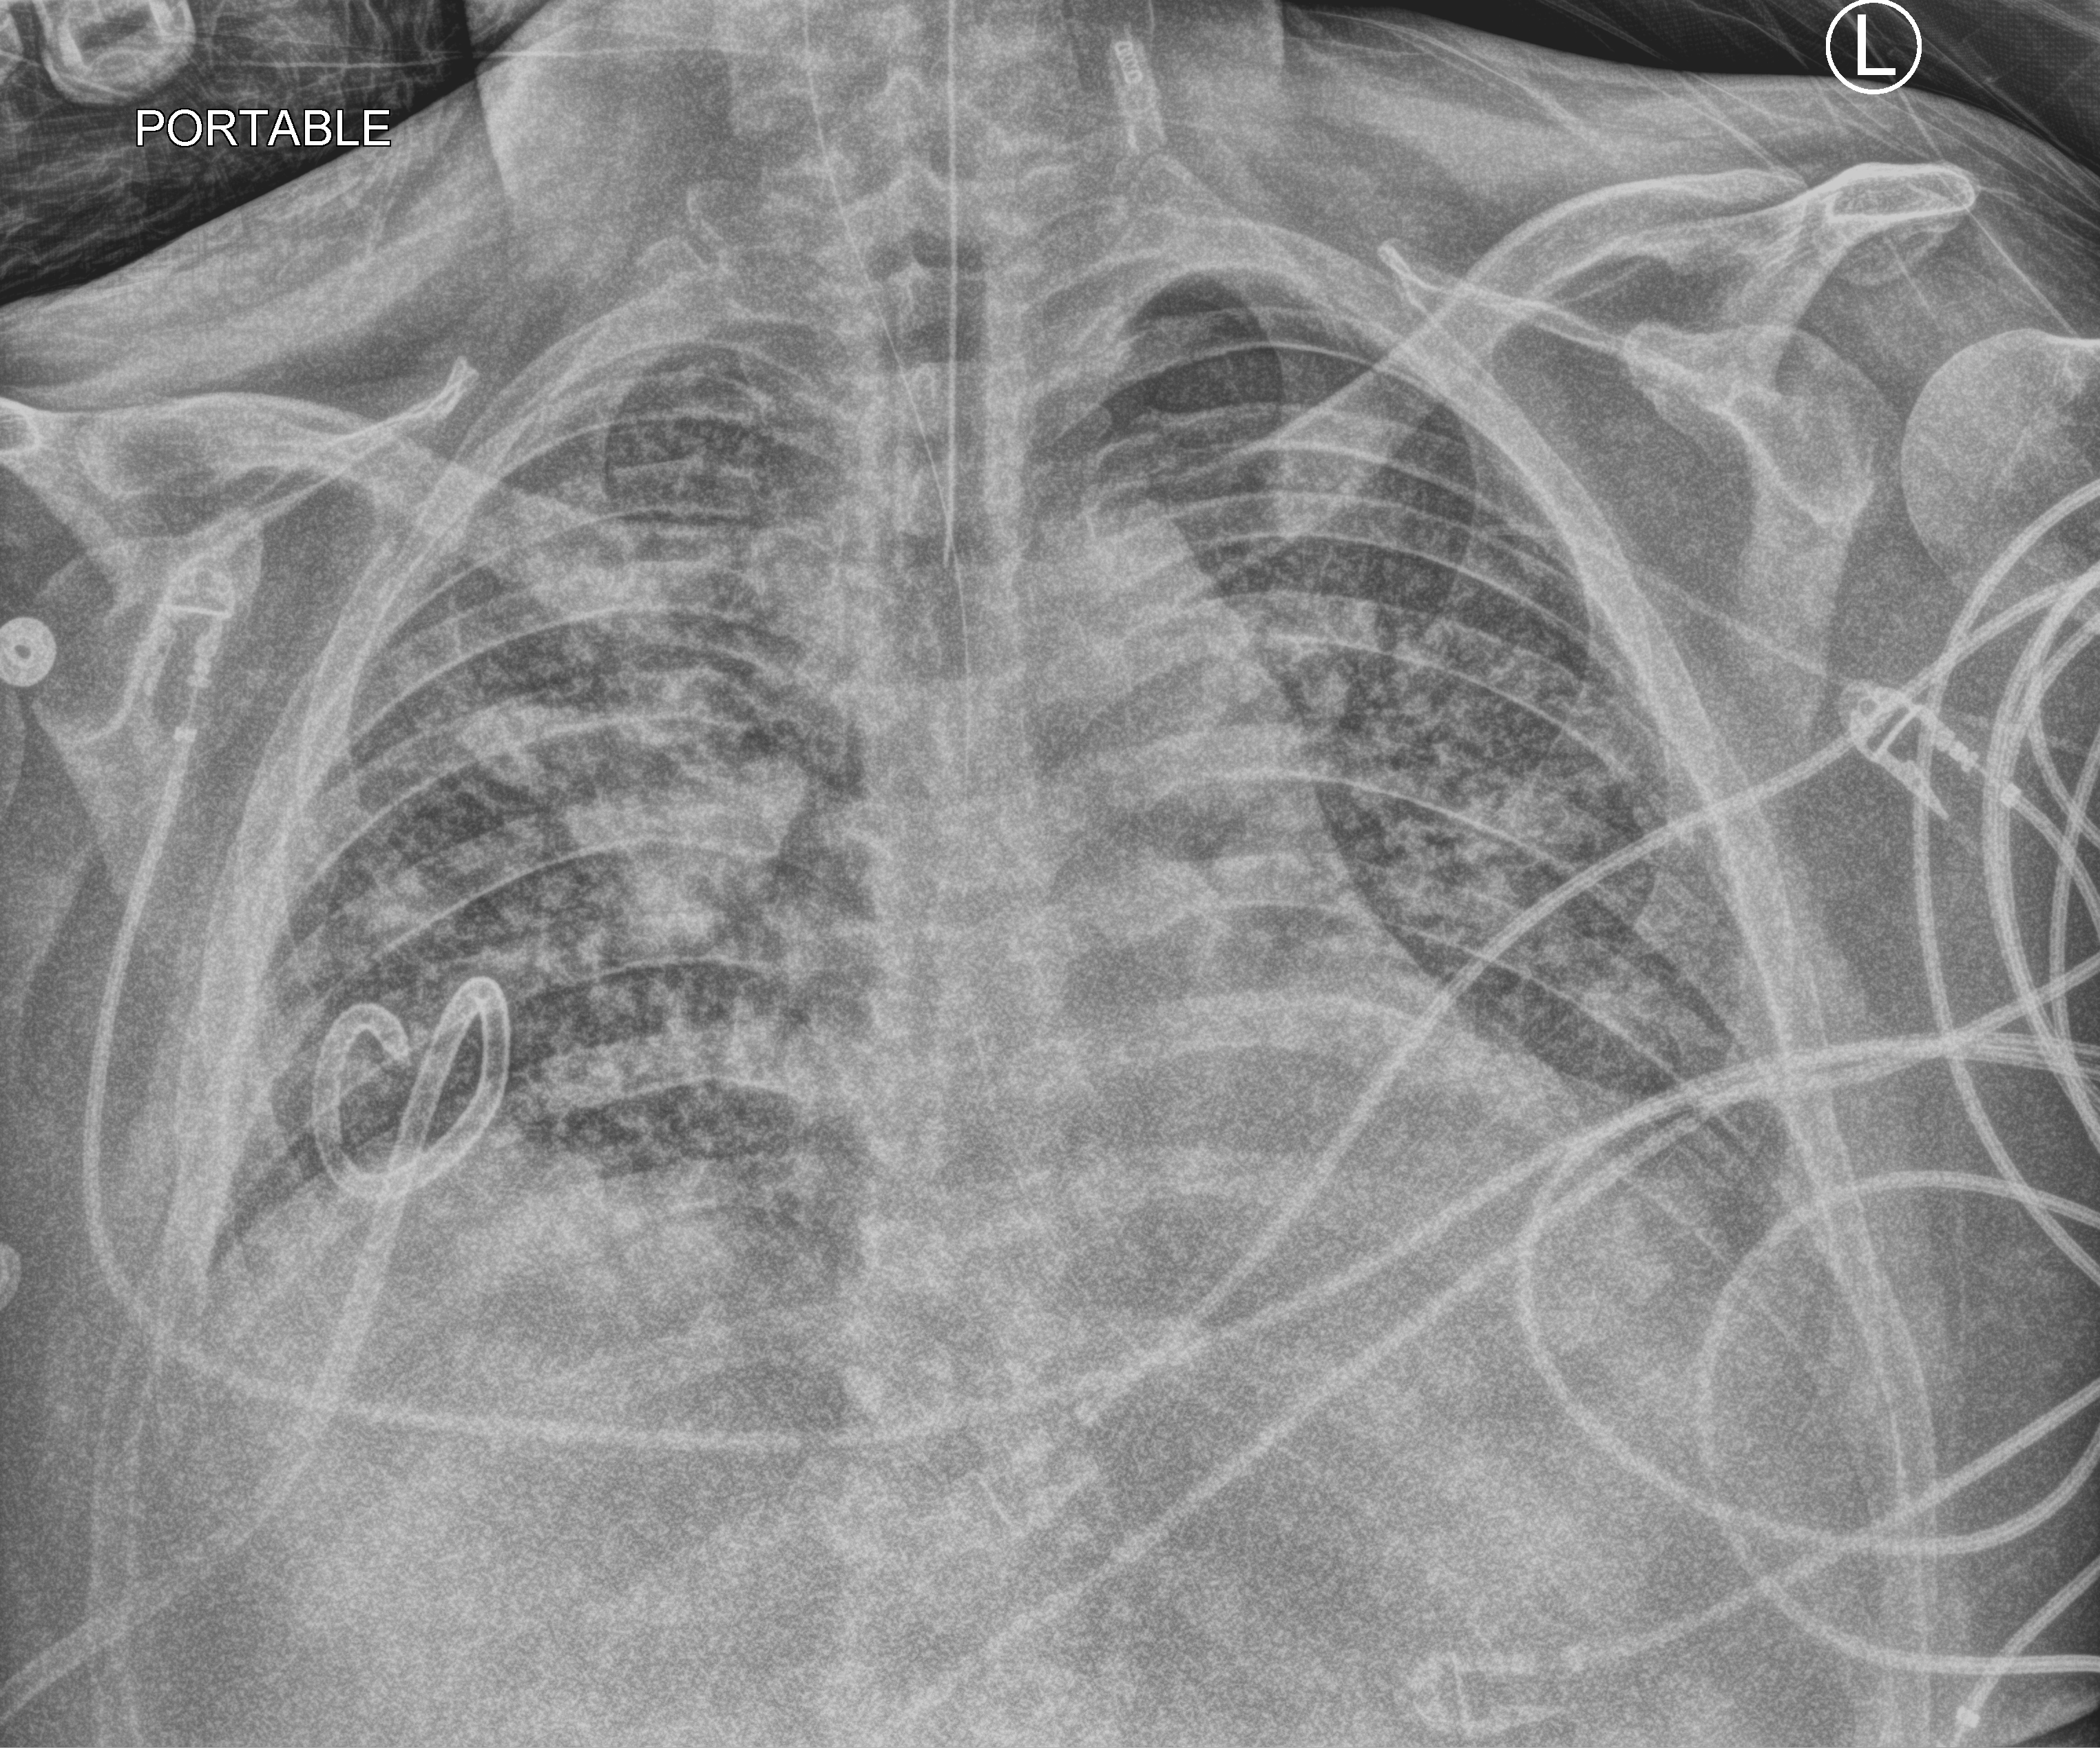
Chest X-ray (portable), anteroposterior (AP) projection. Adult patient hospitalised with COVID-19, age 18–59 years.
Admission-level facts for this patient (not findings on this image; timing relative to this image not recorded): admitted to intensive care during this hospital stay: yes; mechanically ventilated during this hospital stay: yes.